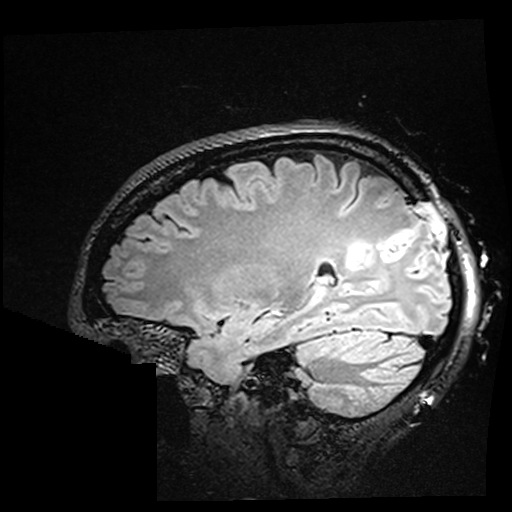
Brain MRI from a brain-tumour surgery series, one sagittal slice. Slice 118 of 176 in the series (ordered by position). T2 FLAIR. 1 mm slice thickness. 512 × 512 image matrix, field of view 250 × 250 mm. Case-level facts recorded for this patient, not image findings: histopathology: Oligodendroglioma; WHO grade: 2; IDH mutation: yes; tumour location: Right Parietal.
Outlined on this slice (manually delineated by an expert):
- residual tumour: bounding box (x1, y1, x2, y2) in pixels: (345, 240, 389, 276)